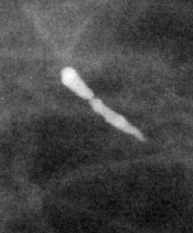
Cropped region of a digitized screen-film mammogram centred on a radiologist-marked abnormality, right breast, CC view.
- Finding: calcifications, morphology large rodlike, distribution segmental; BI-RADS assessment category 2; benign; no additional work-up was recommended (benign without callback).